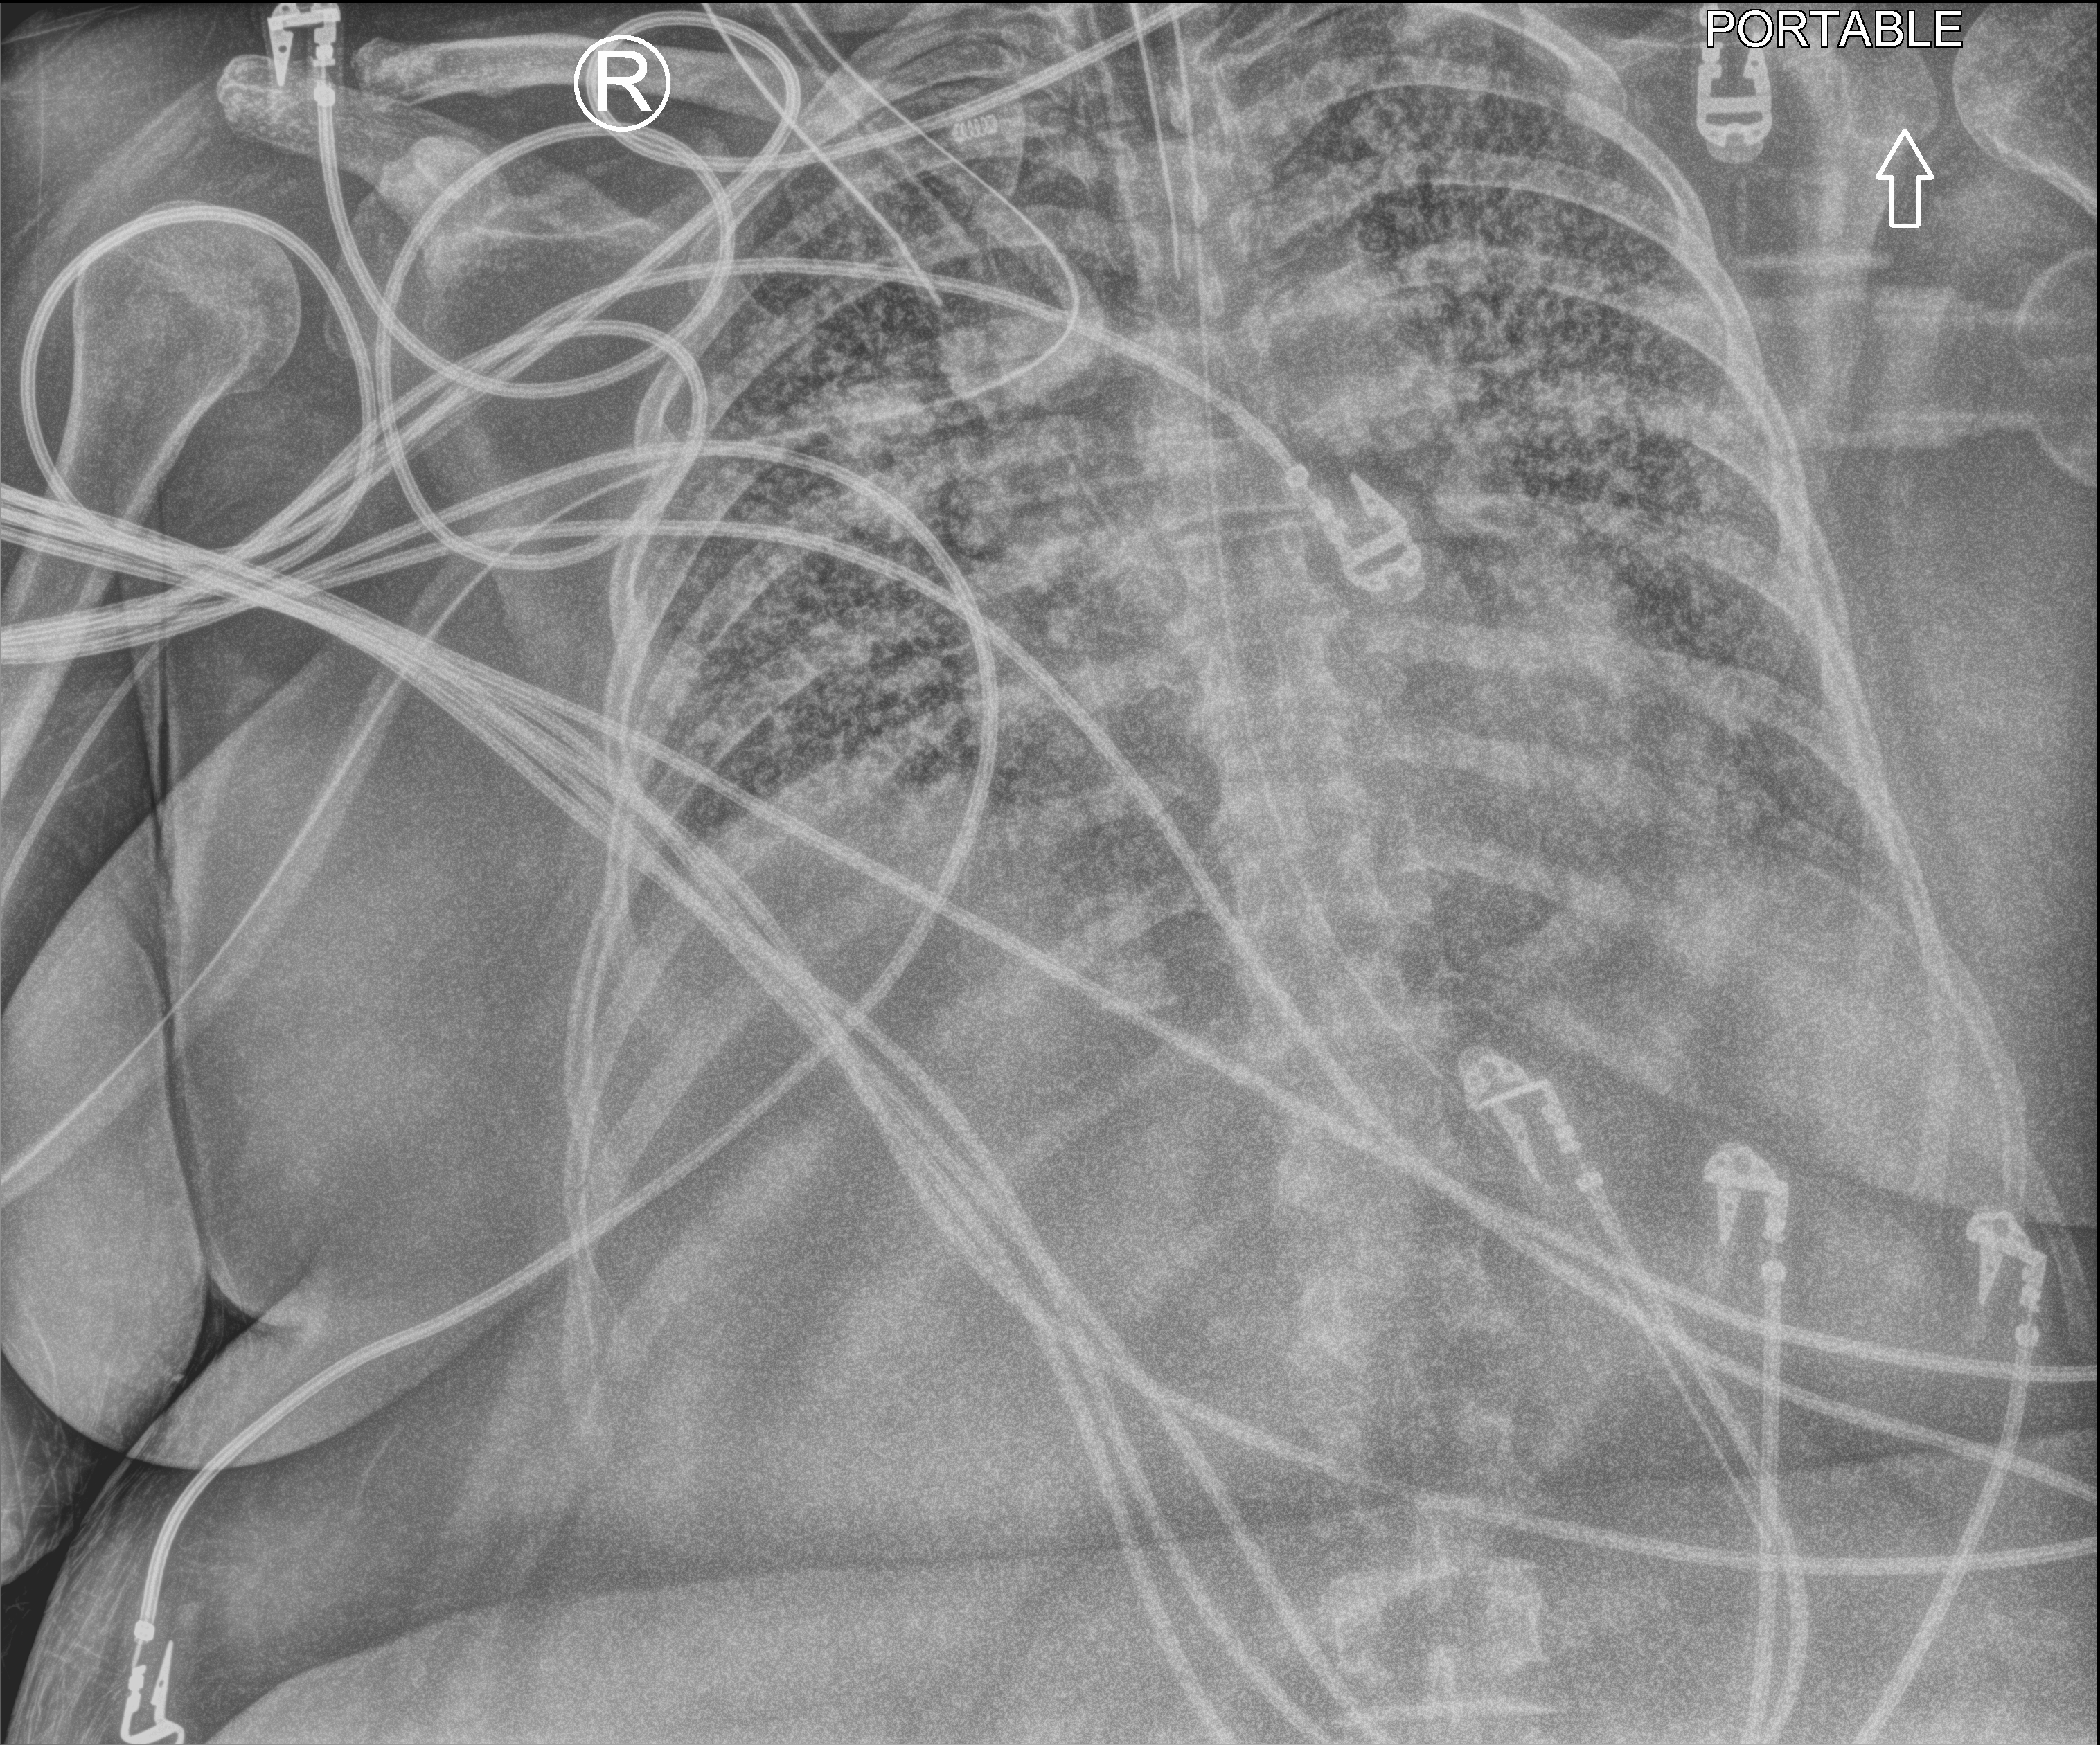
Portable chest radiograph, anteroposterior (AP) projection. Female patient hospitalised with COVID-19, age 18–59 years.
From the hospital-stay record, not from the radiograph (when in the stay this image was taken is not recorded): admitted to intensive care during this hospital stay: yes; hypertension (admission record): yes.